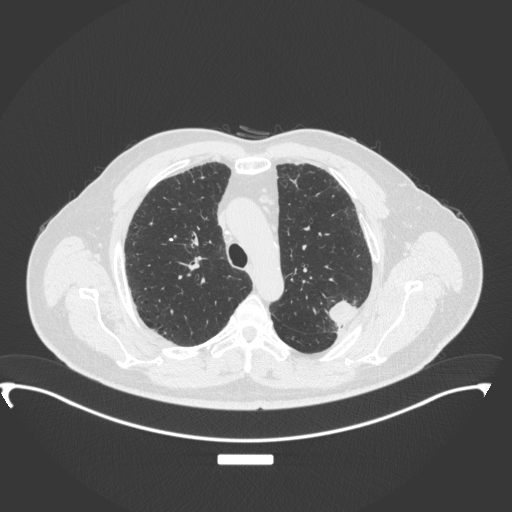
Chest CT, one axial slice. Slice 265 of 350 in the series (ordered by position). 120 kVp. Lung window (W 1500 / L -600 HU). 1 mm slice thickness. 512 × 512 image matrix, field of view 459 × 459 mm. Patient: male, 64 years. From the clinical record (not read from this slice): clinical TNM (as recorded): T1c N1 M1.
Outlined on this slice (bounding box drawn by a radiologist):
- lung tumour (recorded histology: adenocarcinoma): bounding box (x1, y1, x2, y2) in pixels: (322, 290, 362, 330)